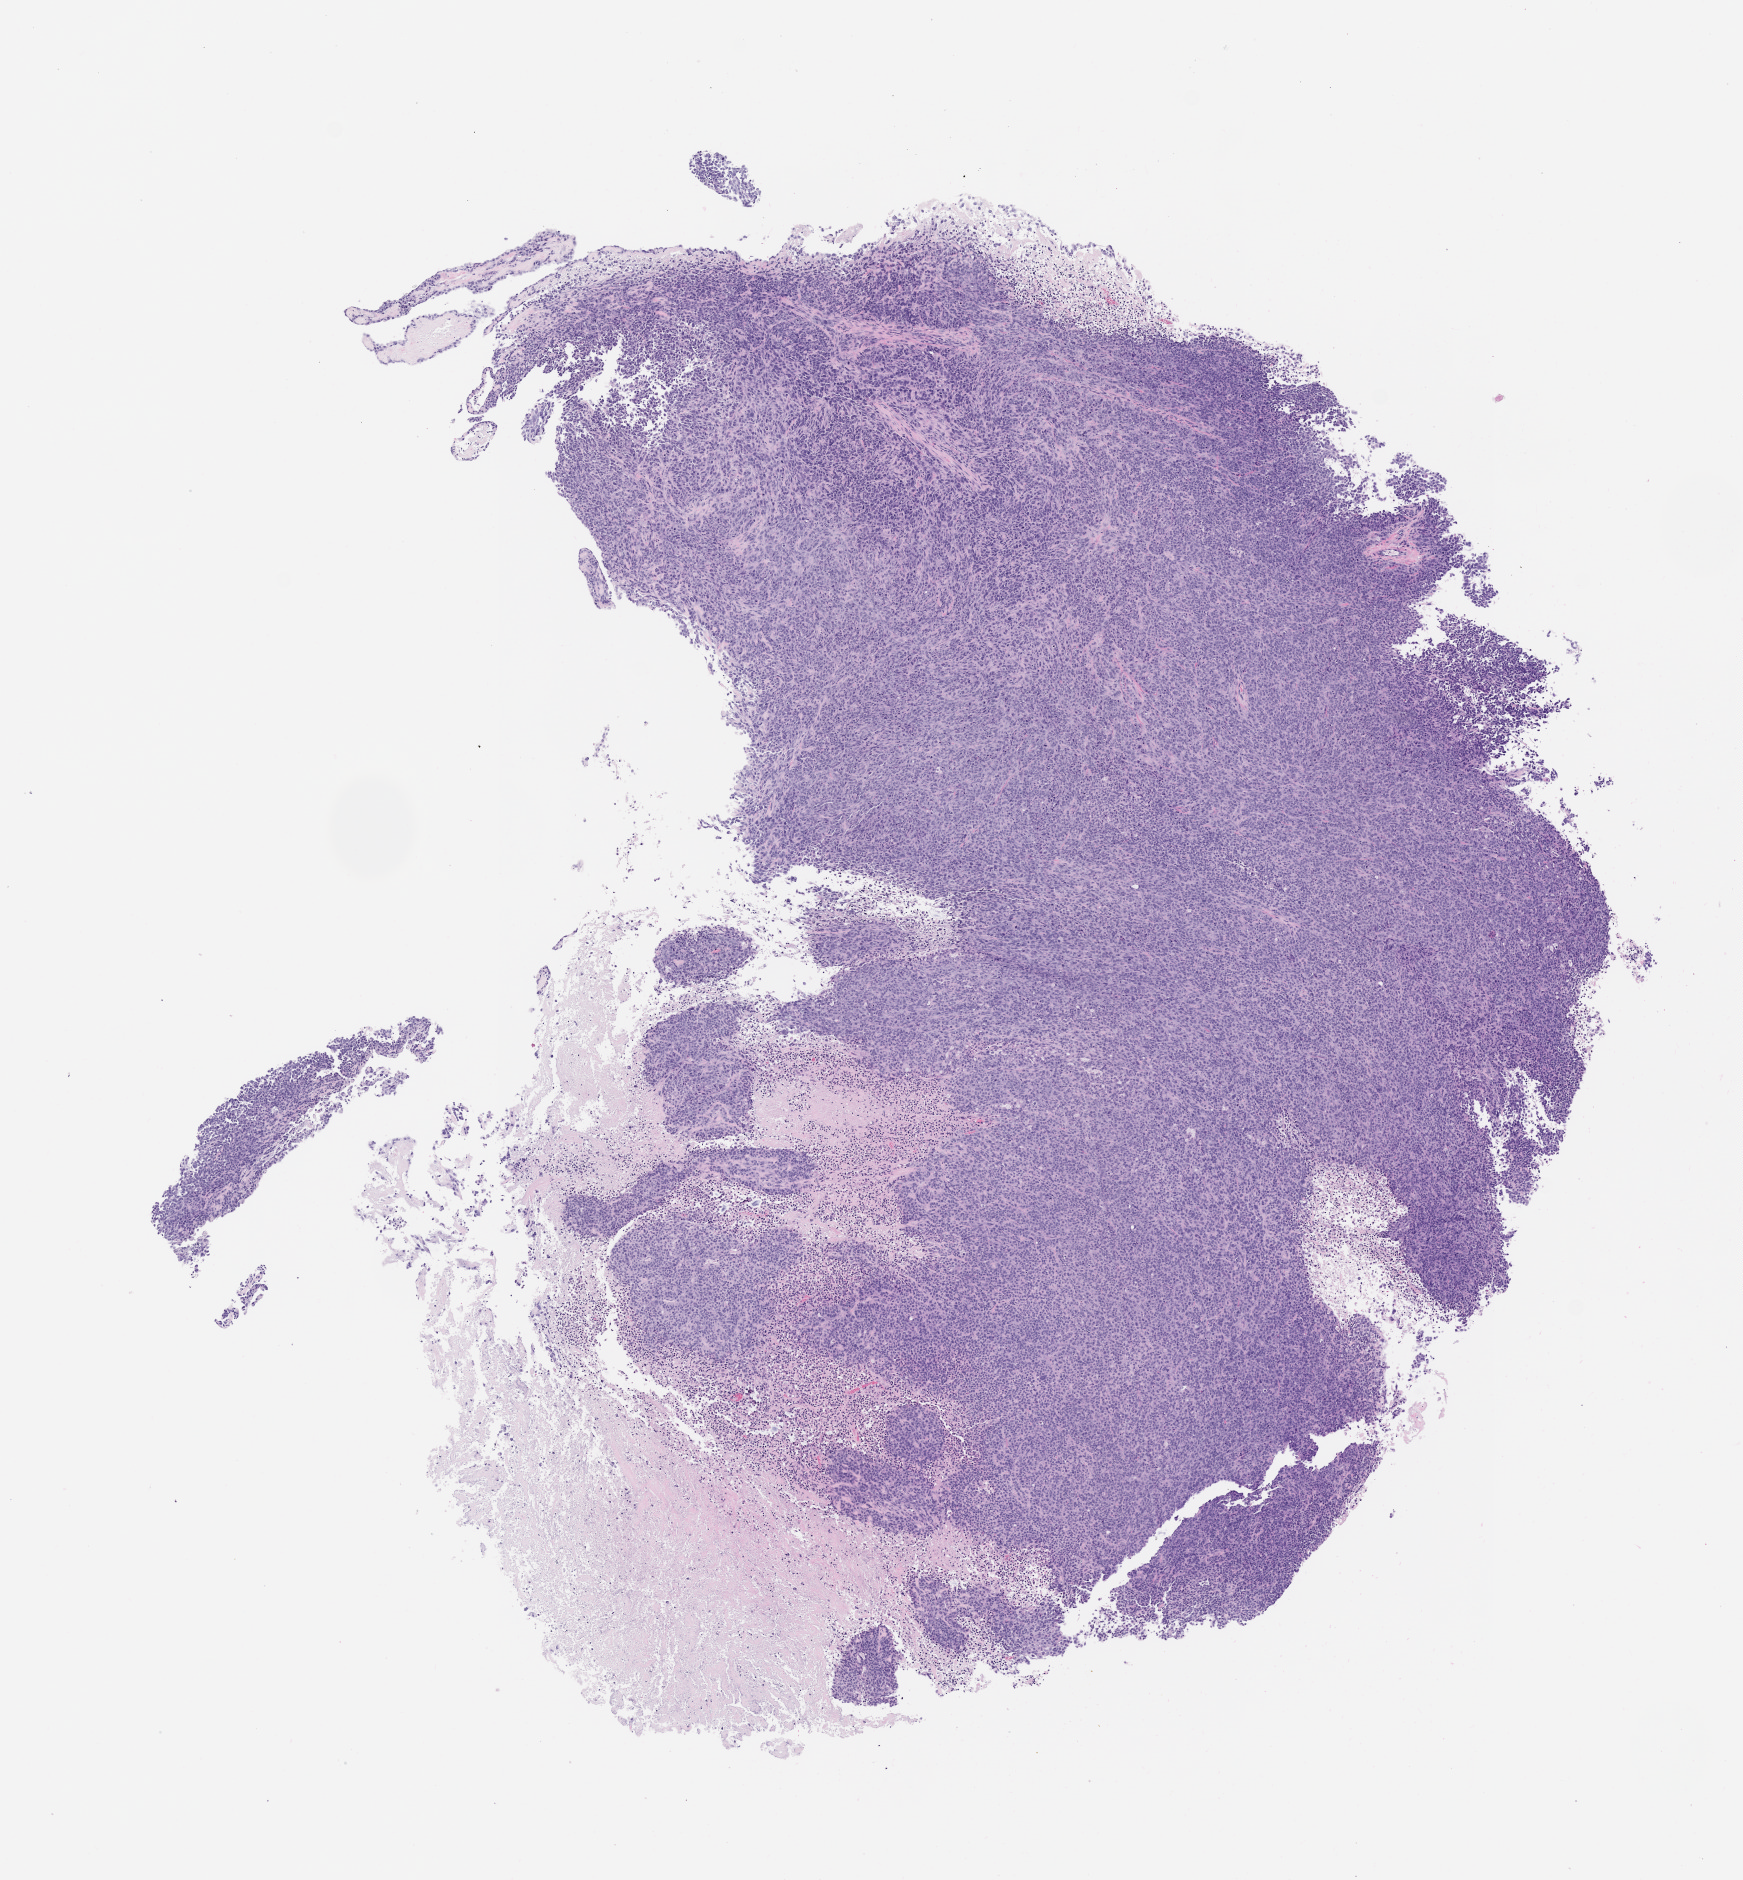
Hematoxylin and eosin (H&E) whole-slide image of a patient-derived xenograft (PDX) tumor grown in a mouse, passage 0, a low-resolution overview of the entire scanned area, about 7.0 x 7.6 mm. Formalin-fixed paraffin-embedded section. Originating tumor site category: pancreas.
Originating patient diagnosis: Pancreatic Adenocarcinoma.